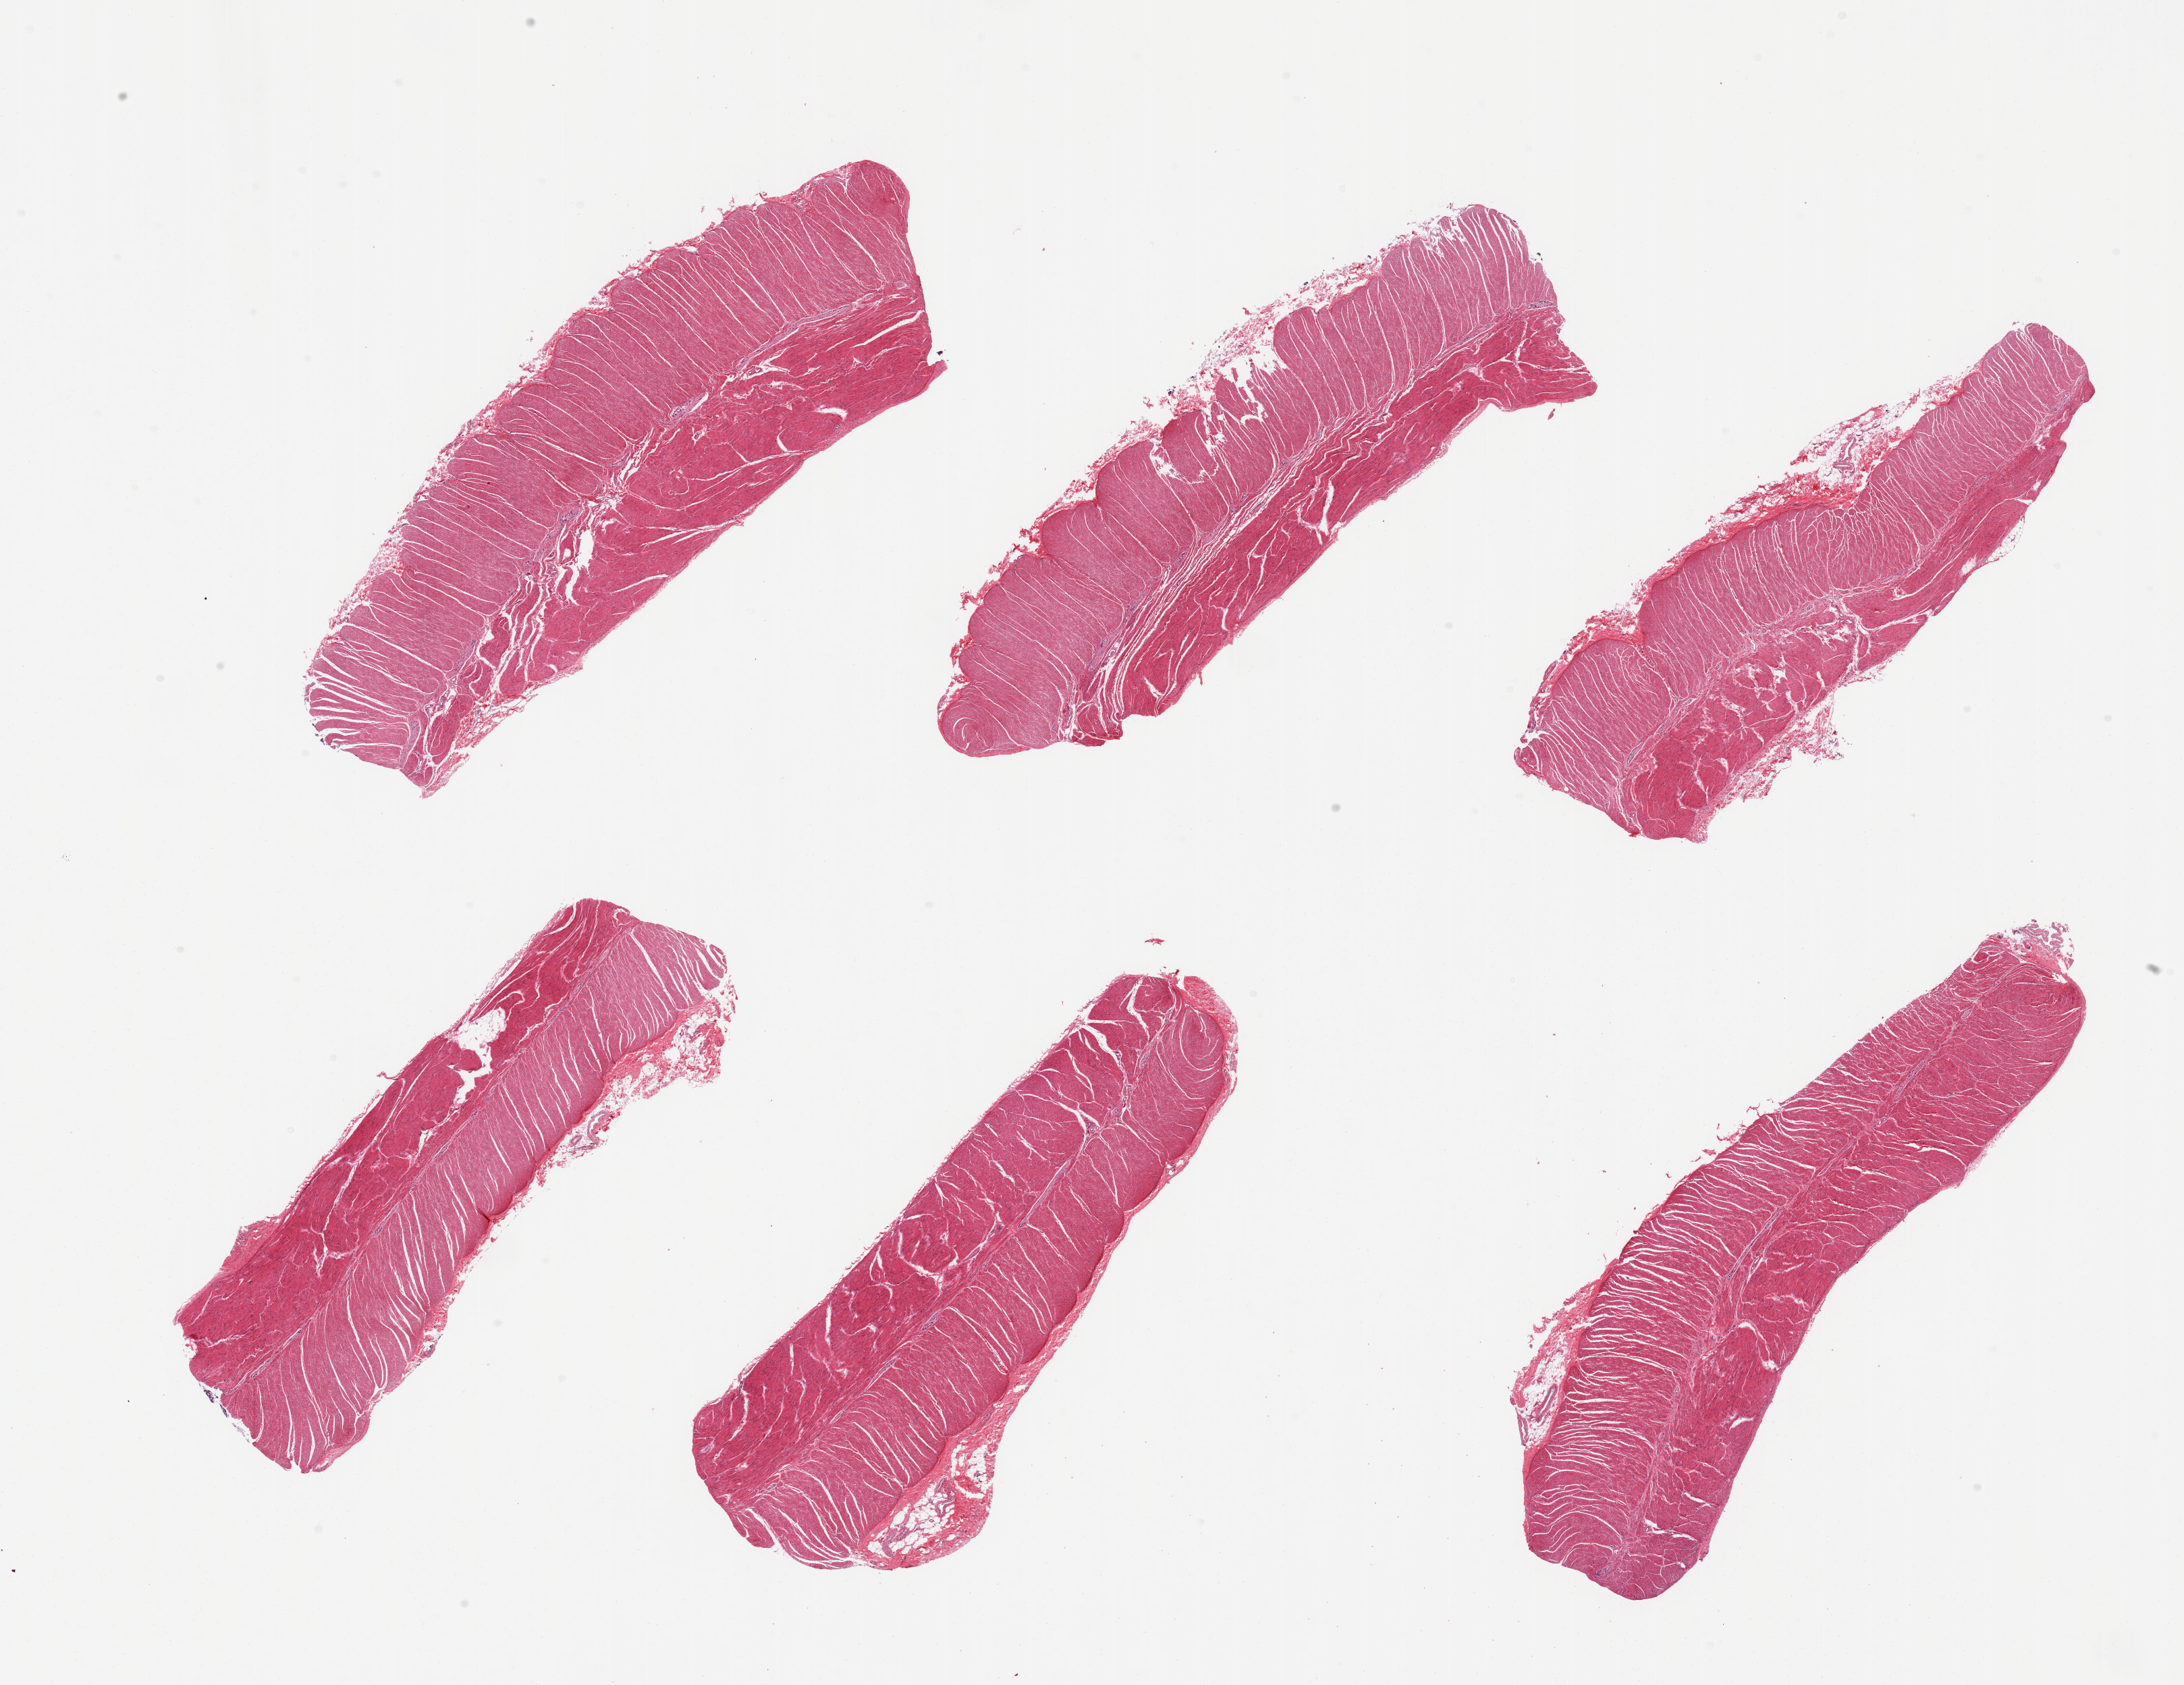
Digitized haematoxylin and eosin-stained section — whole scanned area (about 25.6 x 19.7 mm, from a 20x scan) shown as a low-resolution overview. PAXgene-fixed, paraffin-embedded tissue. Target tissue: sigmoid colon. Tissue donor sample. Male donor.
Reviewer comment on this tissue sample: 6 pieces; target muscularis, well trimmed with minimal attached fat.